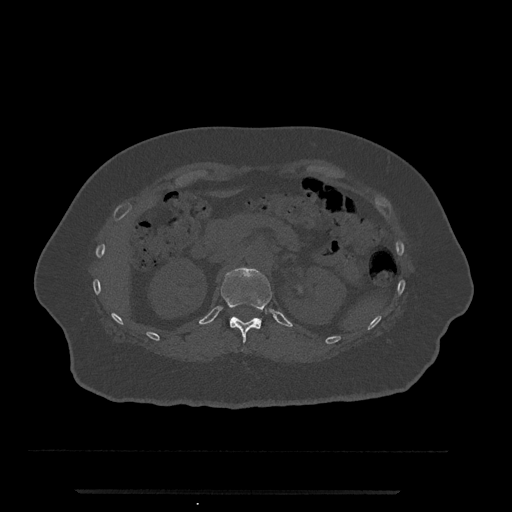
CT including the spine, one axial slice; position 161 of 797 along the scan axis; bone window (W 1800 / L 400 HU); 0.5 mm slice thickness; 512 × 512 image matrix. Patient: female, 51 years. From the clinical record (not read from this slice): primary cancer: neuro.
Outlined on this slice (semi-automatic segmentation, software-assisted and operator-edited):
- T12 vertebra: bounding box <221,267,272,342> (left, top, right, bottom; pixels)